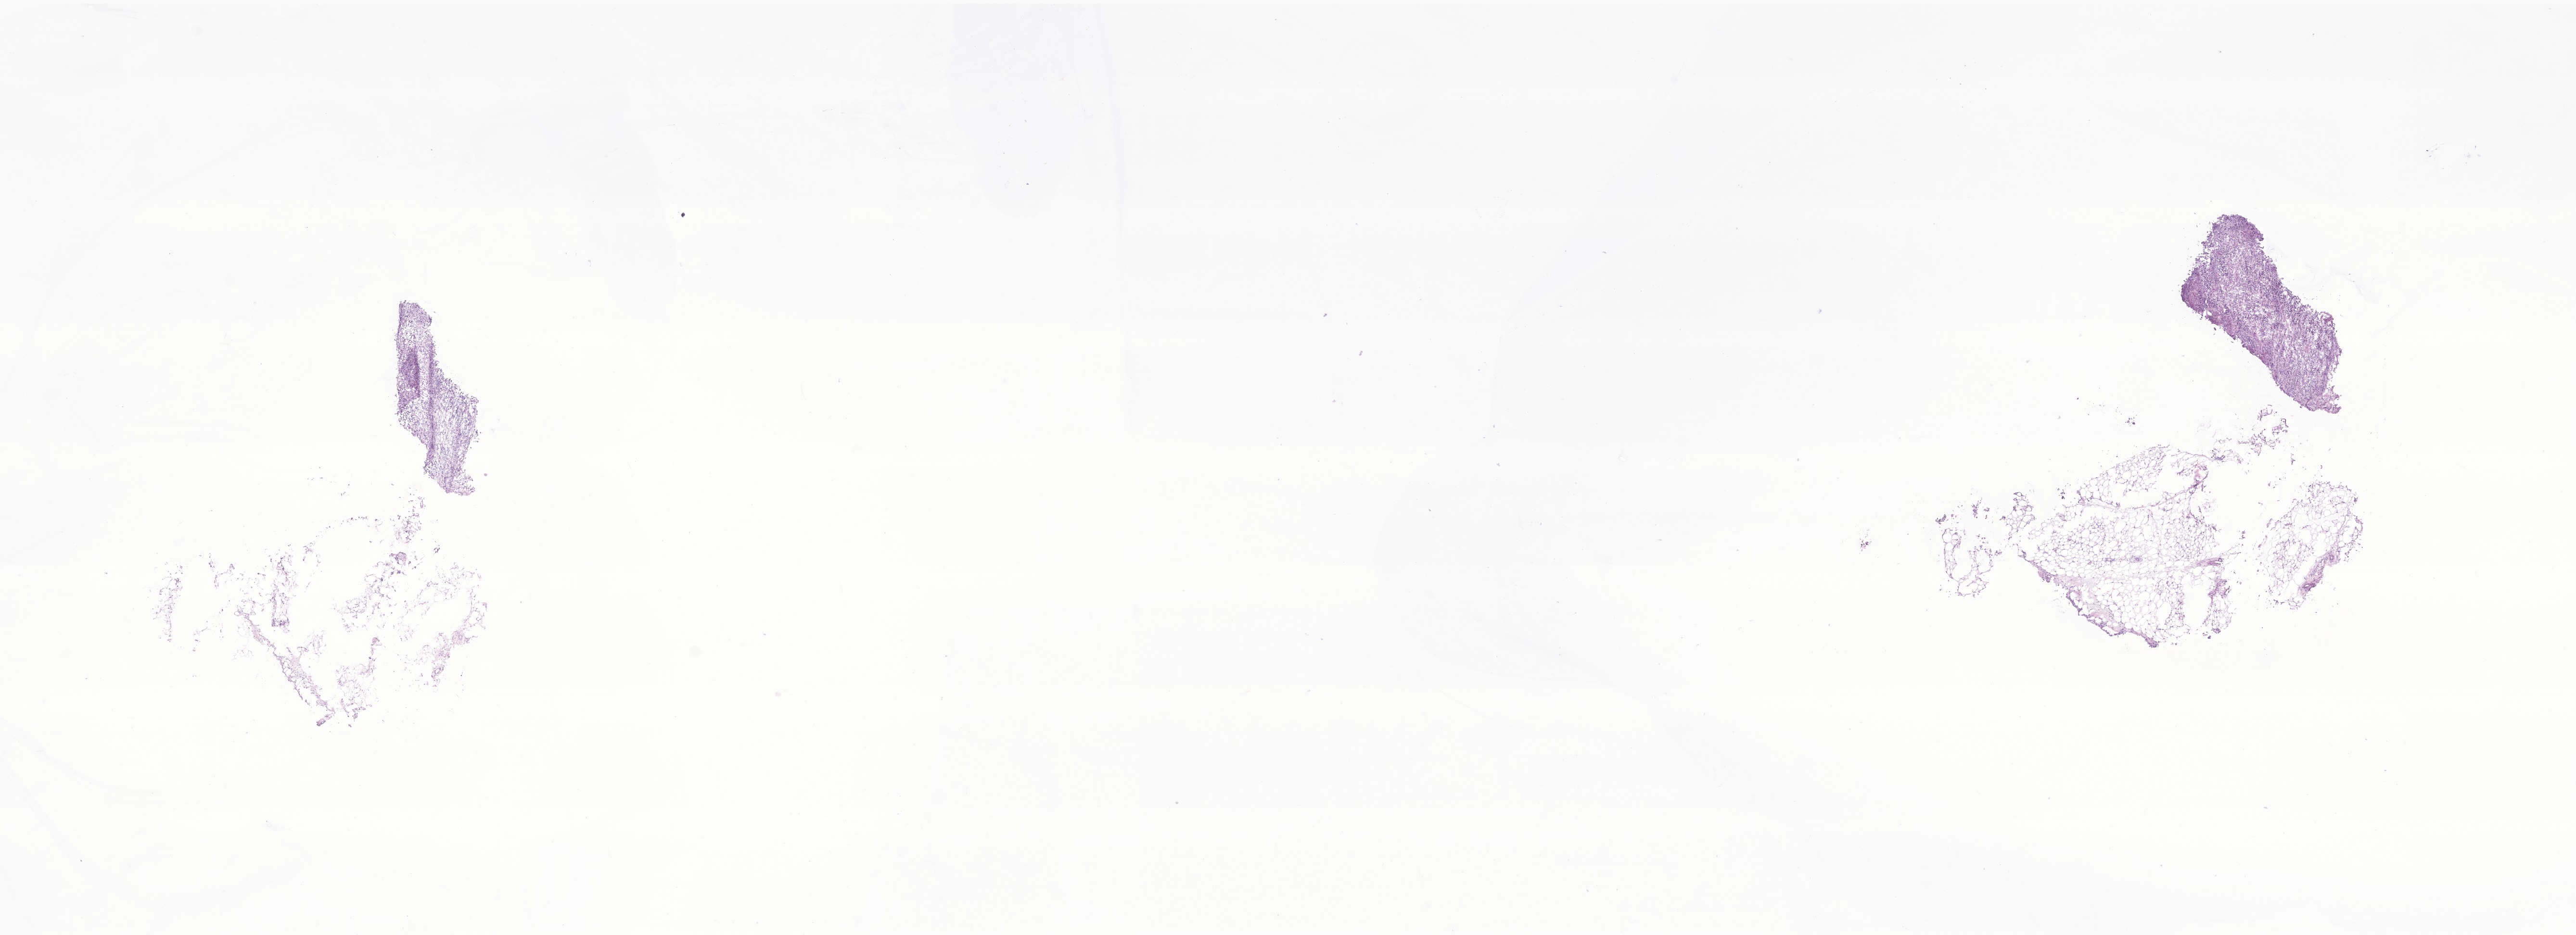
Digitized hematoxylin and eosin (H&E)-stained section of tumor tissue from the soft tissue of lower extremity, whole scanned area (about 22.6 x 8.2 mm) shown as a low-resolution overview; frozen section. Patient male; age 214 months (17 years 10 months).
* tissue or organ of origin (case record): connective, subcutaneous and other soft tissues of lower limb and hip
* diagnosis: Alveolar rhabdomyosarcoma